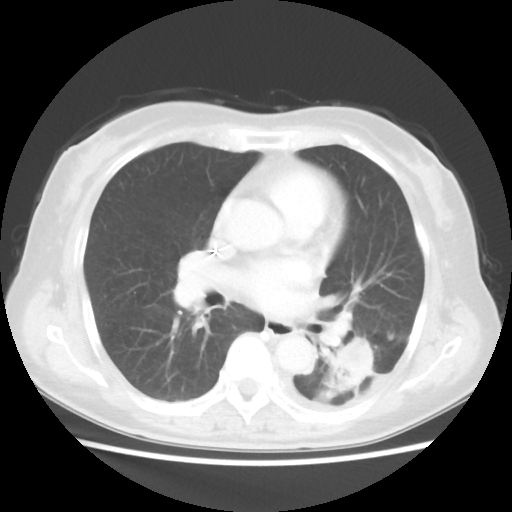
Chest CT, one axial slice; reconstruction kernel STANDARD; 100 kVp; lung window (W 1500 / L -600 HU); 5 mm slice thickness; 512 × 512 image matrix, field of view 341 × 341 mm. Patient: female, 69 years. Case-level facts recorded for this patient, not image findings: clinical TNM (as recorded): T1c N0 M0.
Outlined on this slice (bounding box drawn by a radiologist):
- lung tumour (recorded histology: adenocarcinoma): bounding box (x1, y1, x2, y2) in pixels: (334, 337, 378, 398)